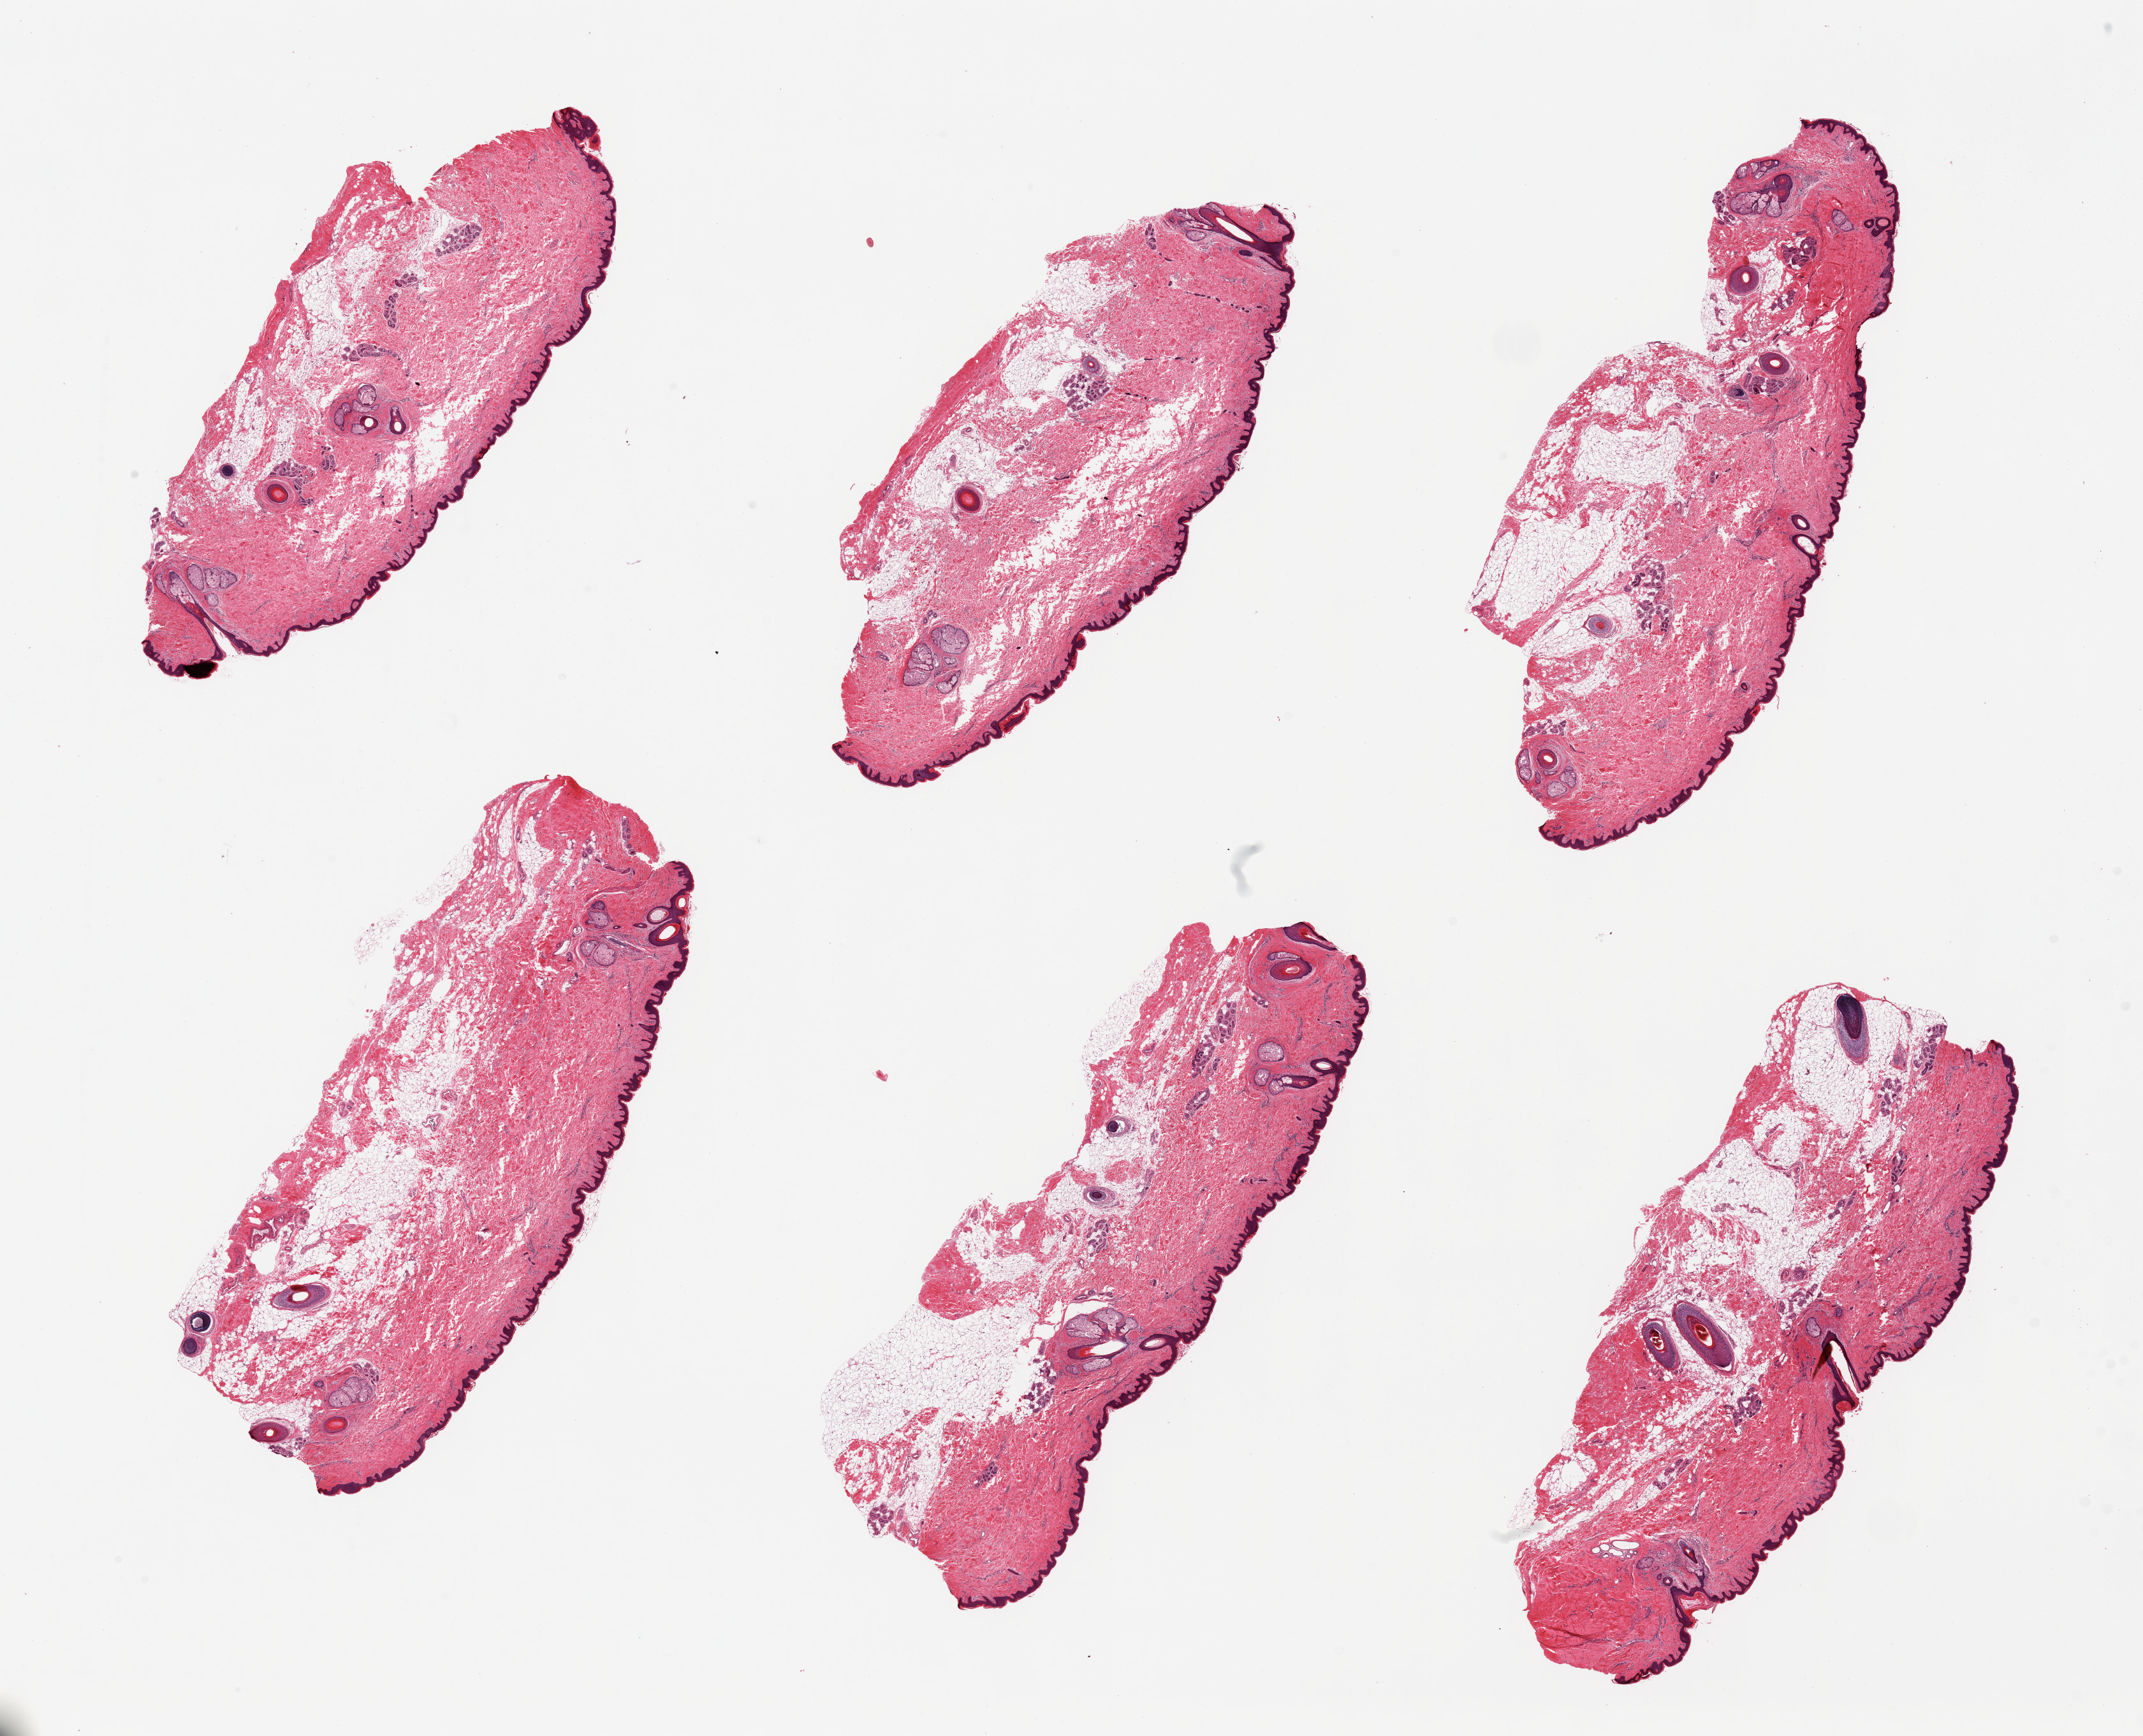
Haematoxylin and eosin whole-slide image — shown as a low-resolution overview of the whole scanned area (about 26.6 x 21.5 mm). PAXgene-fixed, paraffin-embedded tissue. Section of skin of suprapubic region (target tissue). Tissue donor sample.
Reviewer comment on this tissue sample: 6 pieces; squamous epithelium is ~80 micron thick; minimal adherent fat.